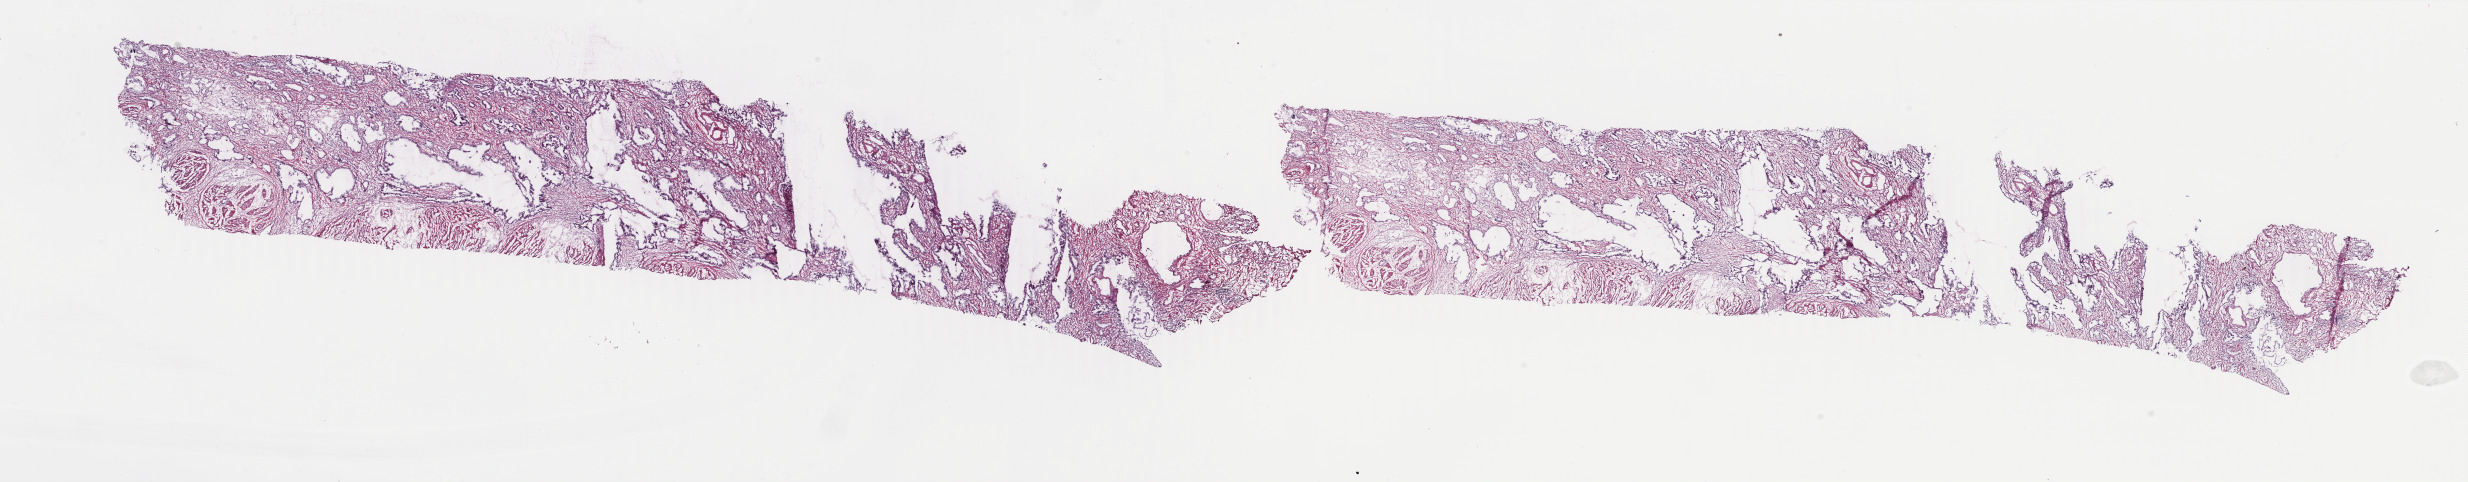
Digitized Hematoxylin and eosin (H&E) stained tissue section (whole slide), low-resolution overview of the scanned area, about 39.3 x 7.7 mm. Frozen section from the top of the tissue portion. Primary tumour sample from the stomach. Patient: female, age at initial diagnosis 69 years. Histologic grade: G2 (moderately differentiated). Composition of this section per pathologist review: tumour cells 45%, tumour nuclei 75%, normal cells 0%, stromal cells 50%, necrosis 5%. Infiltration values recorded for this section: lymphocyte infiltration 4%, monocyte infiltration 0%, neutrophil infiltration 0%.
- AJCC pathologic stage: IIA (7th edition)
- diagnosis: Adenocarcinoma, NOS (cardia, NOS)
- TNM: T3 N0 M0